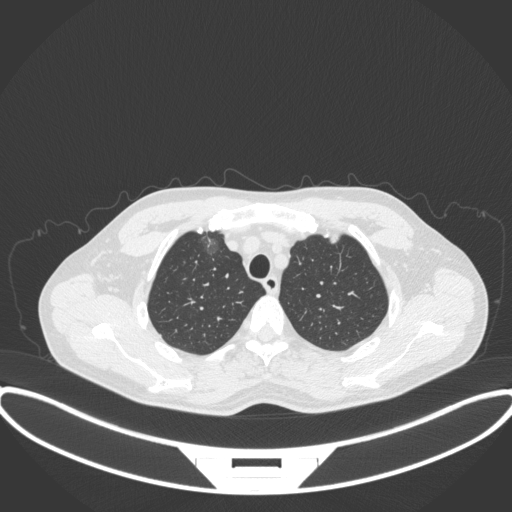
Chest CT, one axial slice; lung window (W 1500 / L -600 HU); 1 mm slice thickness; 512 × 512 image matrix, field of view 424 × 424 mm. Patient: male, 60 years. Case-level facts recorded for this patient, not image findings: clinical TNM (as recorded): T1c N0 M0.
Annotated regions visible in this slice (rectangle marked by the reading radiologist):
- lung tumour (recorded histology: adenocarcinoma): bounding box <203,227,223,261> (left, top, right, bottom; pixels)